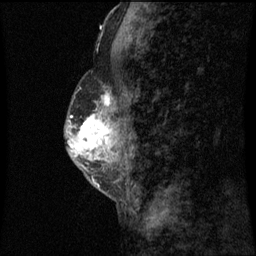
Breast MRI (dynamic contrast-enhanced), one sagittal slice. Position 26 of 60 along the scan axis. Dynamic contrast-enhanced series, image 2 of 3 at this slice position (ordered by acquisition). 1.5 T. TE 4.2 ms, TR 8.9 ms. 256 × 256 image matrix. Female patient, age 50 years. Case-level facts recorded for this patient, not image findings: setting: breast cancer imaged before/during neoadjuvant chemotherapy; receptor status: triple-negative.
Outlined on this slice (semi-automatic segmentation, software-assisted and operator-edited):
- analysis volume of interest (the breast-tissue region the enhancement analysis was run in; not a lesion): box from (x=68, y=82) to (x=115, y=169) px
- tumour enhancement mask (voxels above the 70 % enhancement threshold inside the analysis volume of interest): (x=71, y=94)–(x=111, y=155)